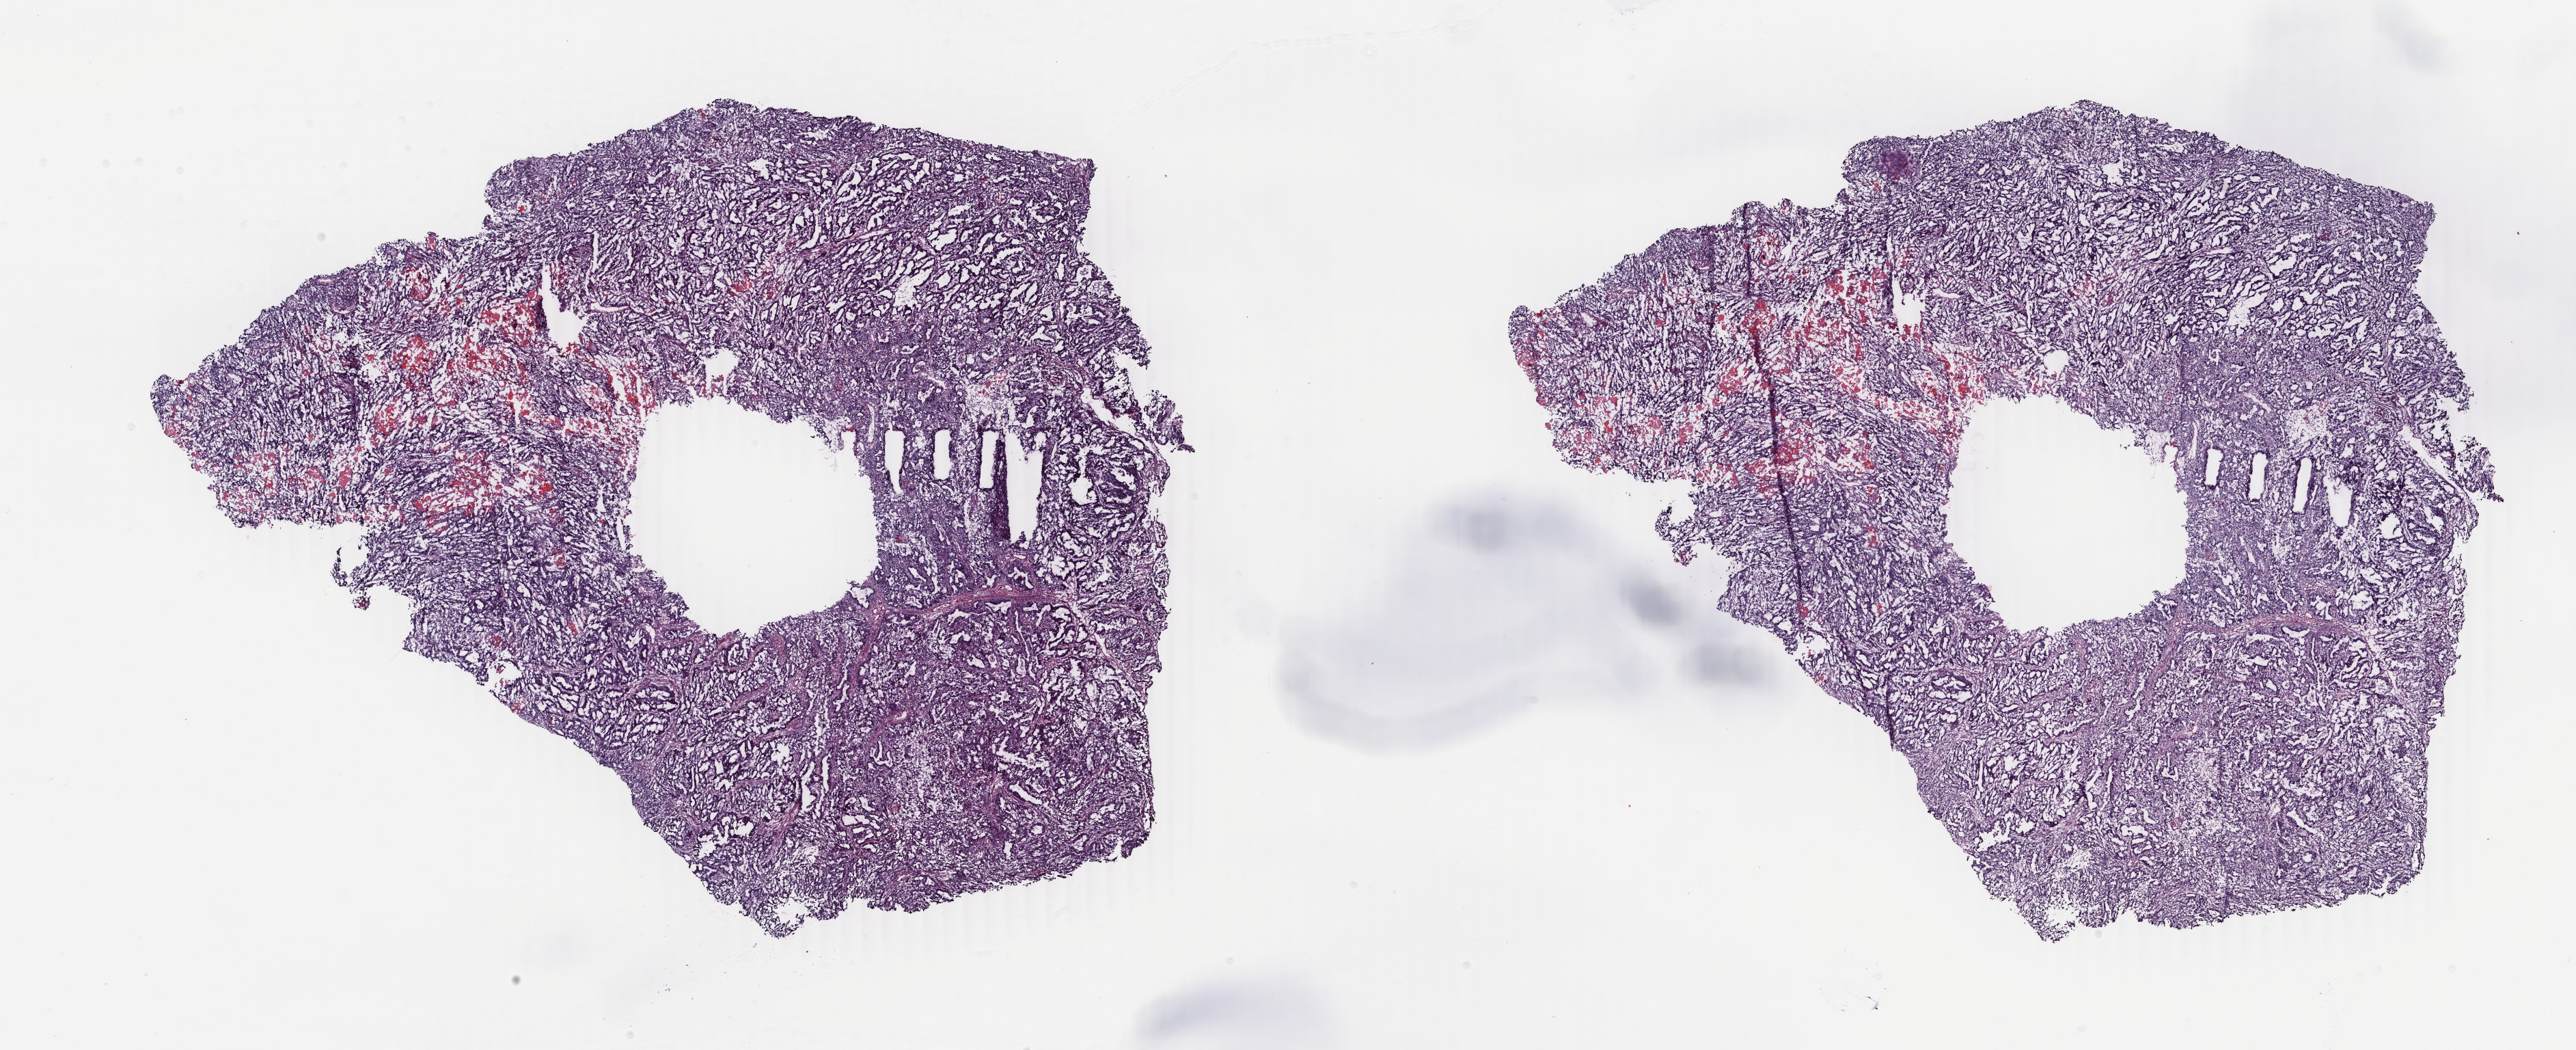
Hematoxylin and eosin (H&E) stained whole-slide image, shown as a low-resolution overview of the whole scanned area (about 30.0 x 12.2 mm, slide scanned at 40x), frozen section from the top of the tissue portion, uterus, primary tumour sample. Female patient; age at initial diagnosis 83 years. Slide review estimates, as recorded: tumour cells 75%, tumour nuclei 85%.
Histologic diagnosis: Endometrioid adenocarcinoma, NOS (endometrium).